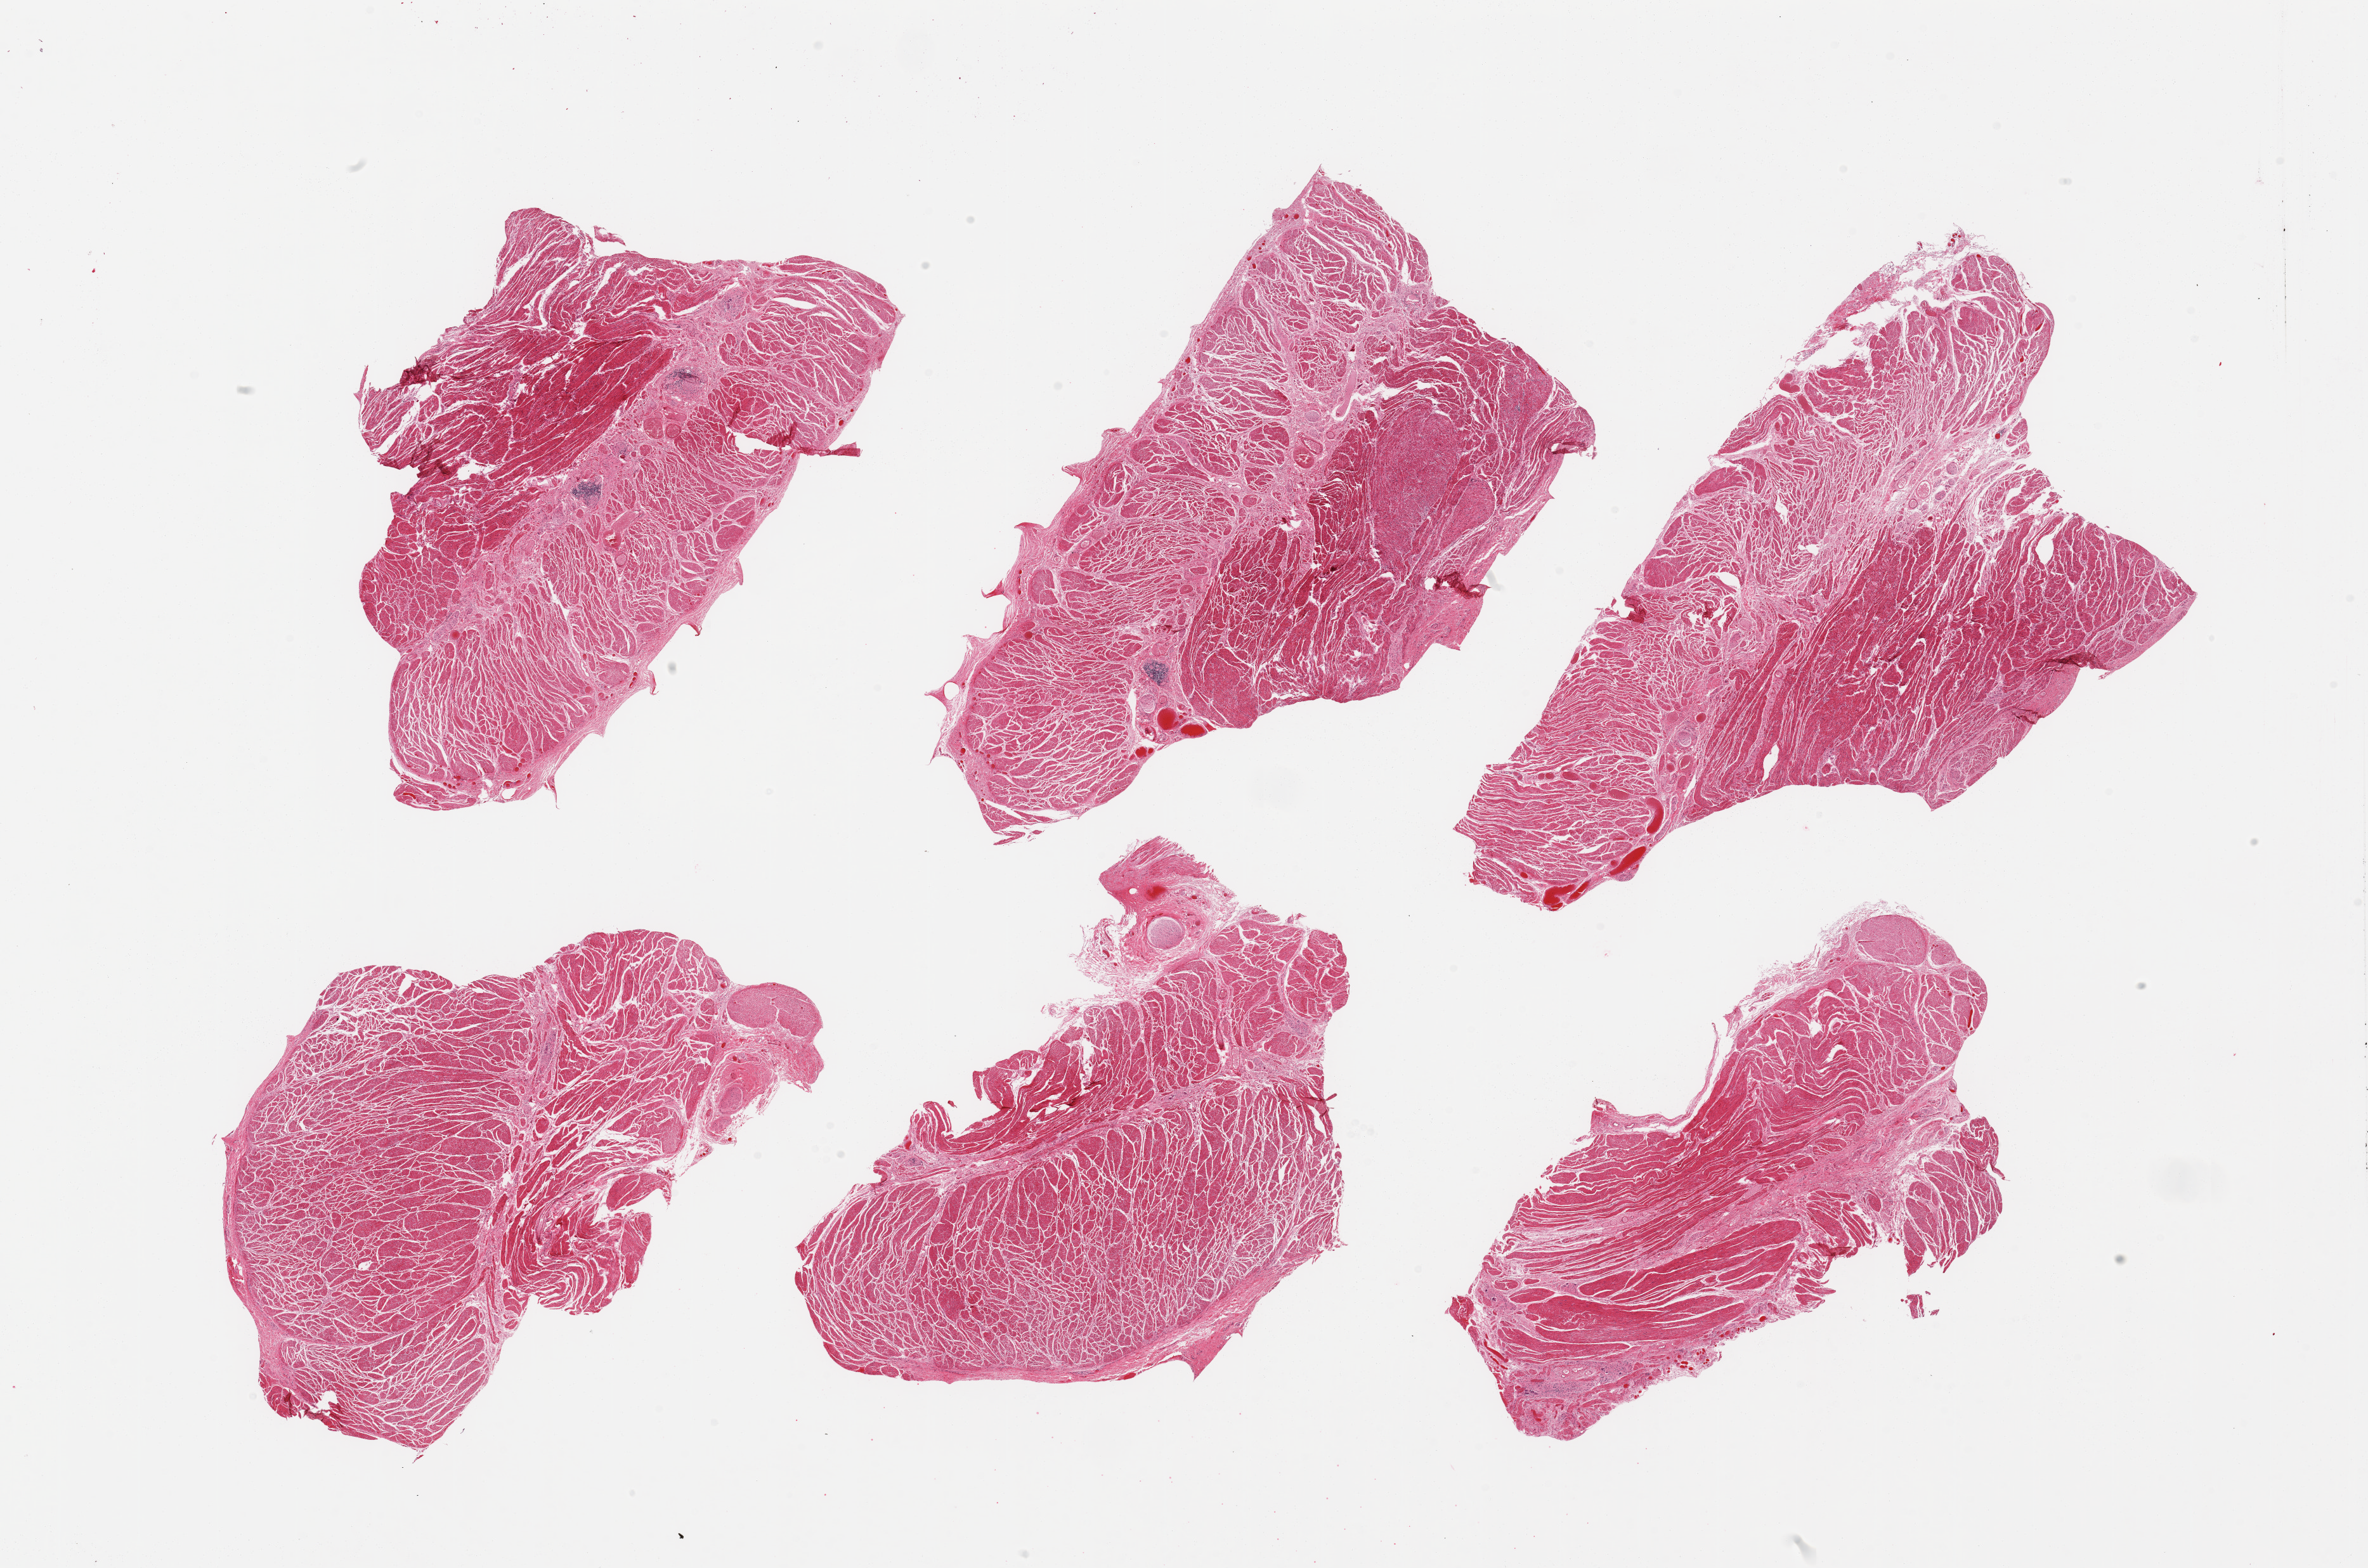
Digitized H&E-stained section — whole scanned area (about 29.5 x 19.6 mm, acquisition: 20x scan) shown as a low-resolution overview. PAXgene-fixed paraffin-embedded (PFPE) section. Section of gastroesophageal junction (target tissue). Donor tissue sample. Male donor.
• pathologist's review note for this sample: 6 pieces; well trimmed target muscularis